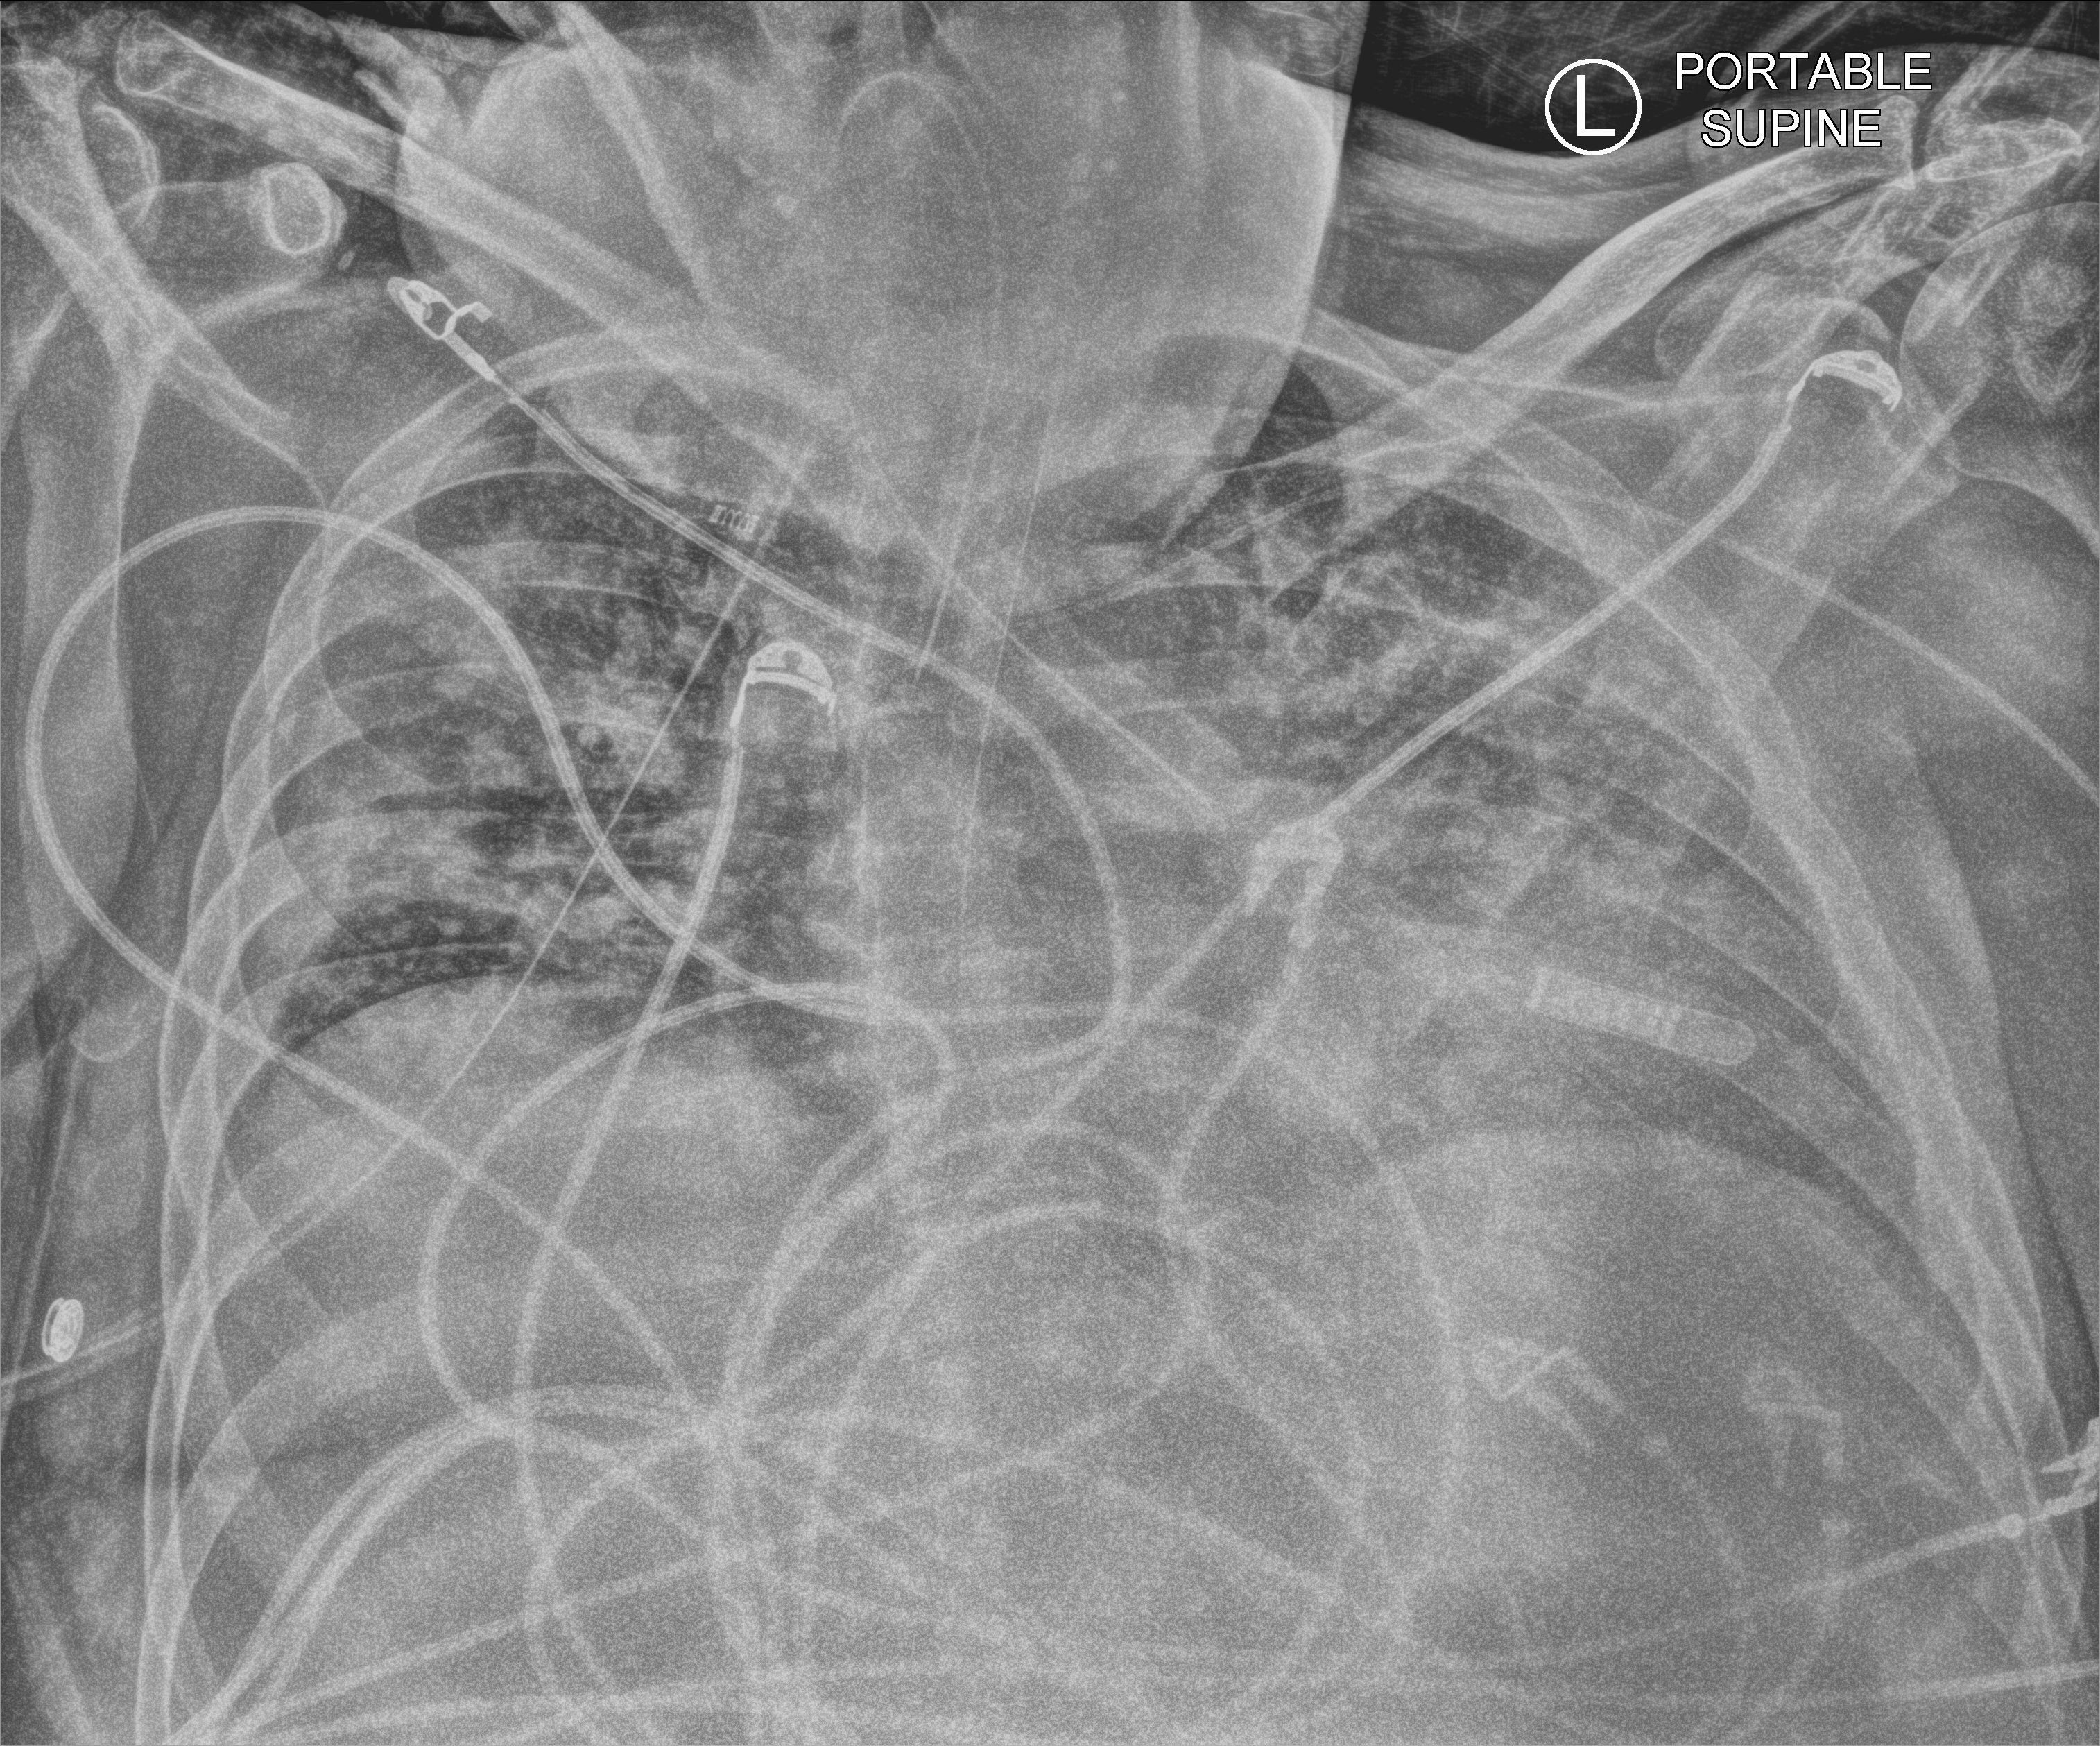
Bedside chest radiograph (computed radiography), anteroposterior (AP) projection. Male patient hospitalised with COVID-19, age 18–59 years.
Admission-level facts for this patient (not findings on this image; timing relative to this image not recorded): other chronic lung disease (admission record): yes; mechanically ventilated during this hospital stay: yes; admitted to intensive care during this hospital stay: yes.